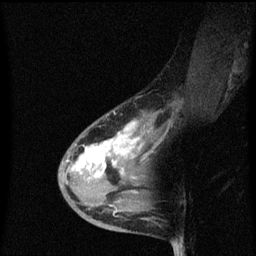
Breast MRI (dynamic contrast-enhanced), one sagittal slice; position 30 of 60 along the scan axis; dynamic contrast-enhanced series, image 2 of 3 at this slice position (ordered by acquisition); 1.5 T; TE 4.2 ms, TR 8.4 ms; 256 × 256 image matrix, field of view 200 × 200 mm. Patient: female, 38 years. From the clinical record (not read from this slice): setting: breast cancer imaged before/during neoadjuvant chemotherapy; receptor status: HR-positive, HER2-negative.
Structures marked on this image (semi-automatic segmentation, software-assisted and operator-edited):
- analysis volume of interest (the breast-tissue region the enhancement analysis was run in; not a lesion): bounding box [x1, y1, x2, y2] px = [60, 110, 151, 205]
- tumour enhancement mask (voxels above the 70 % enhancement threshold inside the analysis volume of interest): [72, 122, 143, 177]